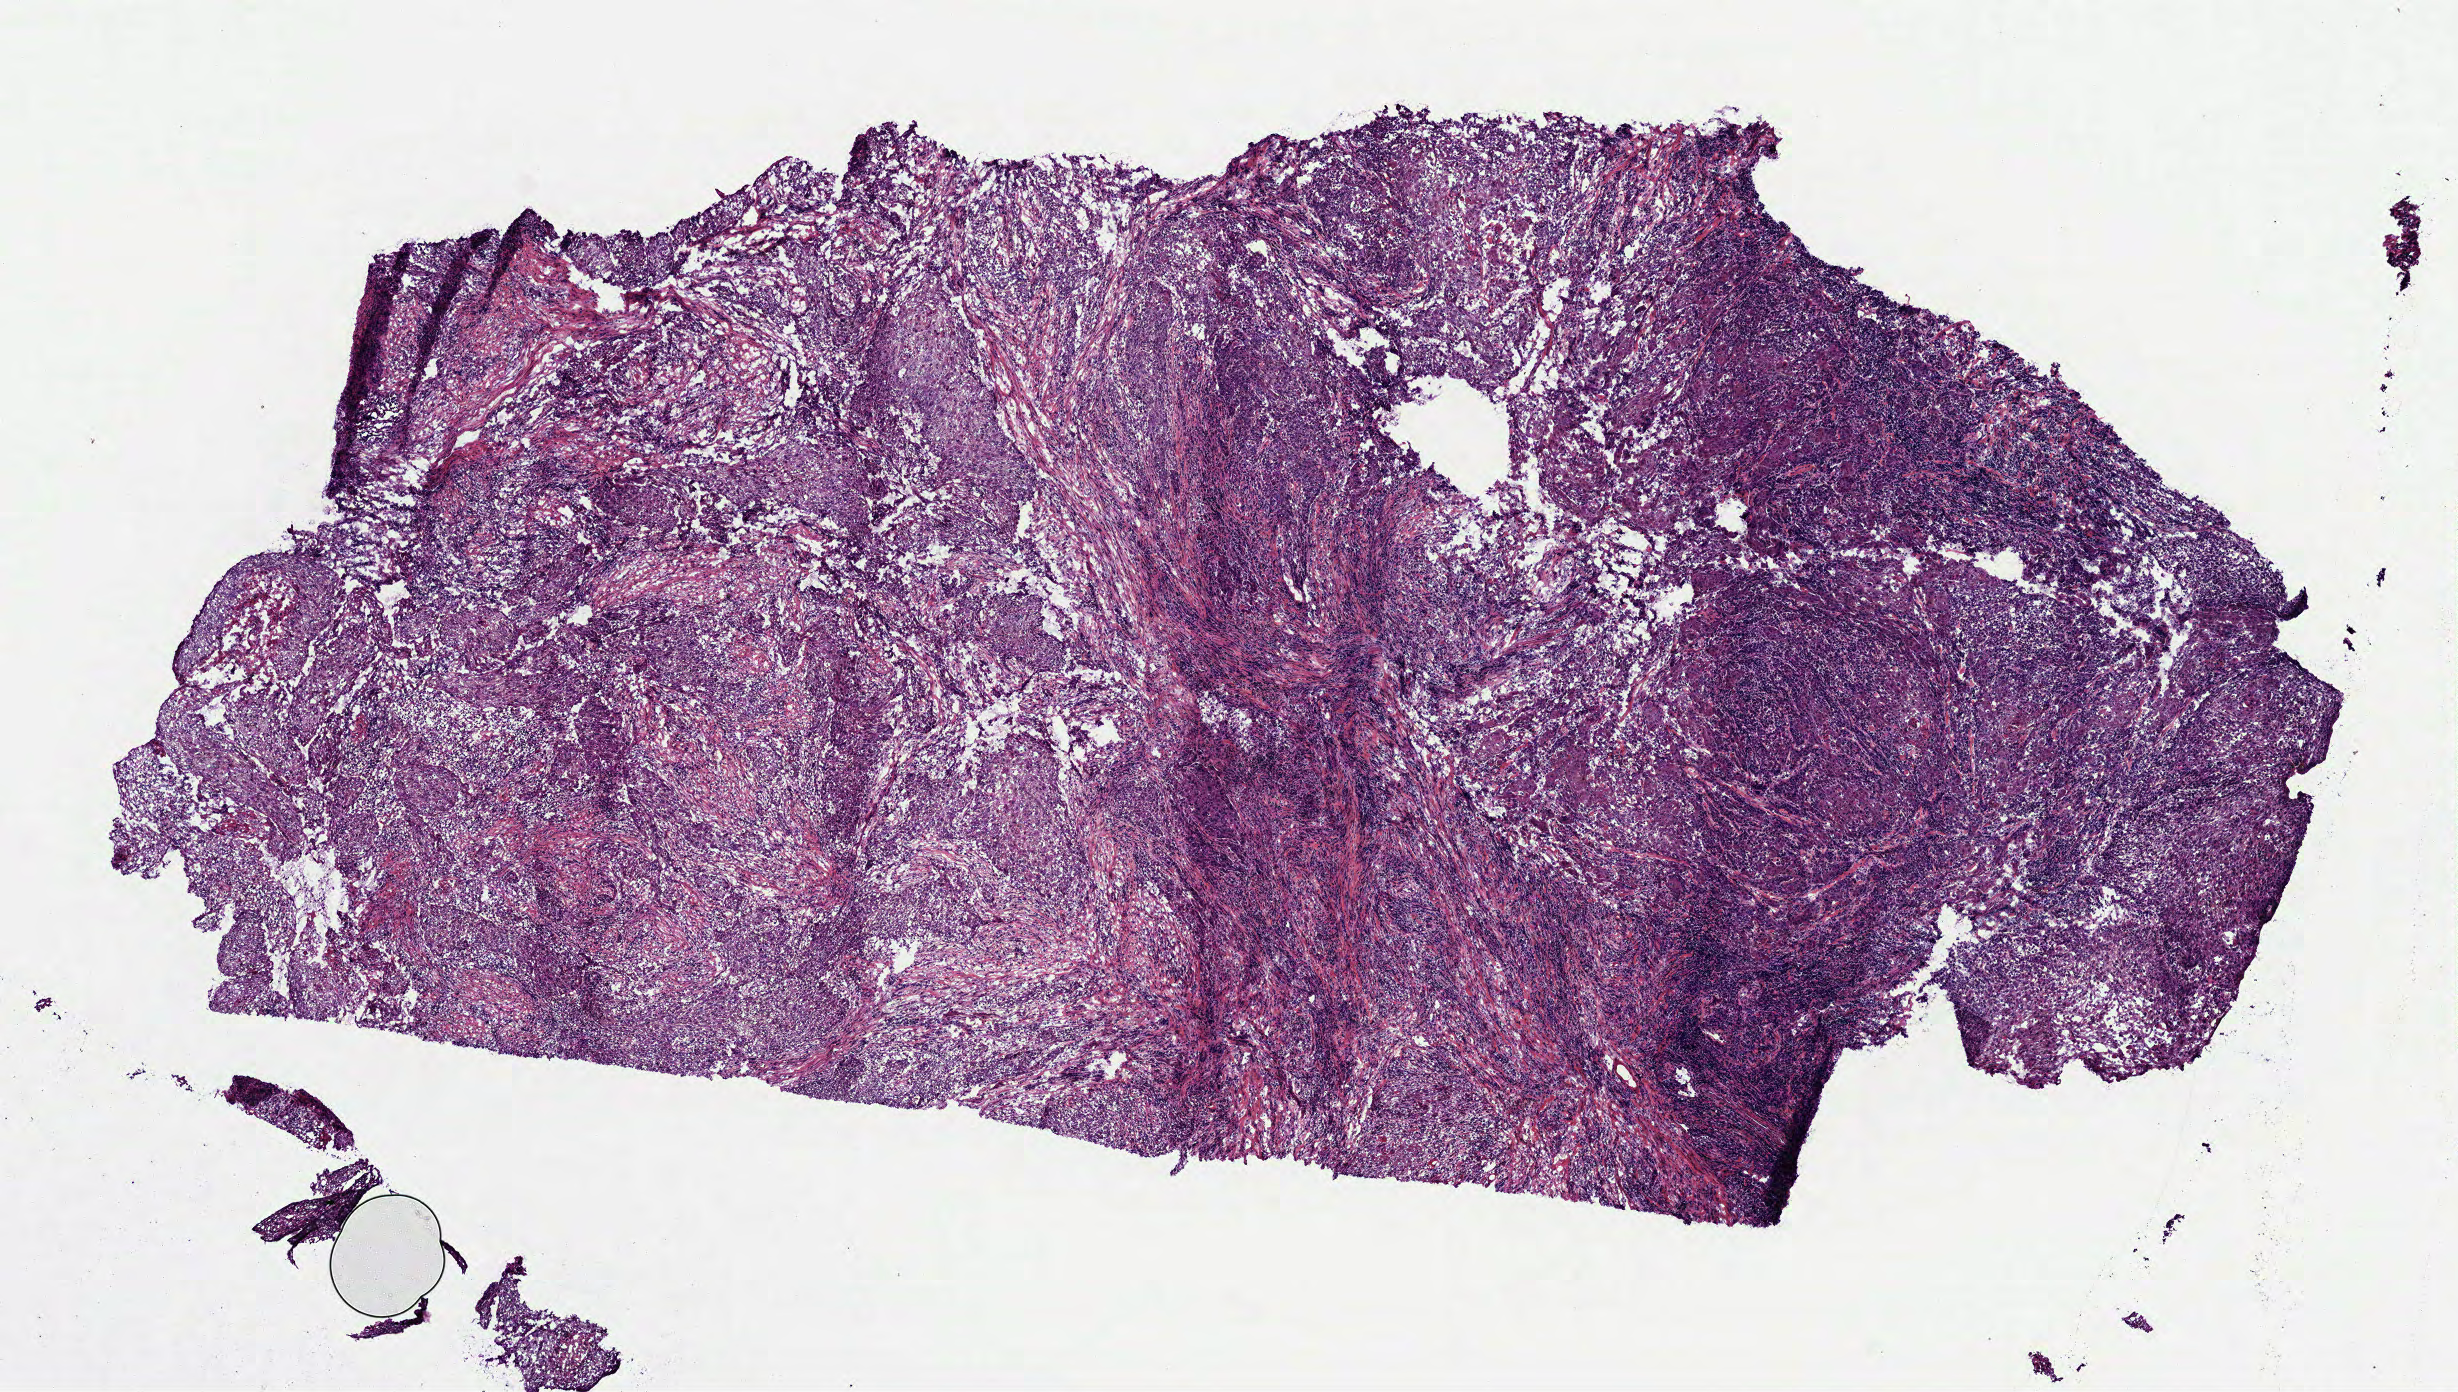
Whole-slide histology image, H&E-stained — a low-resolution overview of the entire scanned area, about 9.9 x 5.6 mm (slide scanned at 40x). Frozen section from the bottom of the tissue portion. Sample: primary tumour, head and neck. Patient: male, age at initial diagnosis 56 years. Histologic grade: G3 (poorly differentiated). Pathologist review of this section (percent, as recorded): tumour cells 85%, tumour nuclei 60%, normal cells 0%, stromal cells 15%, necrosis 0%.
AJCC pathologic stage: IVA. Diagnosis: Squamous cell carcinoma, NOS (gum, NOS).